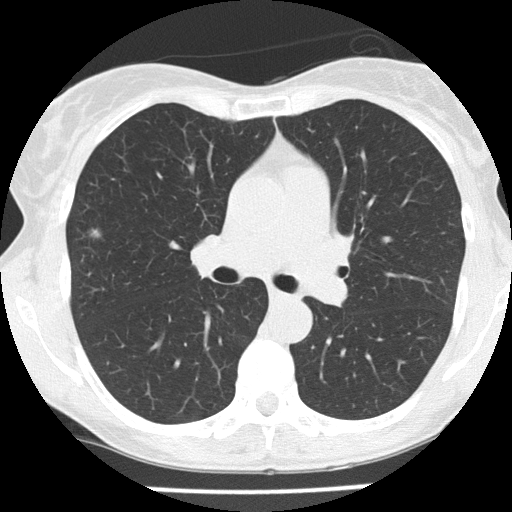
Chest CT (low-dose screening protocol), one axial image; first (baseline) screen; lung window (W 1500 / L -600 HU); 2 mm slice thickness; lung (sharp) reconstruction kernel (FC51); slice 64 of 166 in the series; 512 × 512 image matrix. Female participant, aged 56 years at enrolment. Former smoker at enrolment.
Expert-annotated lung lesion, bounding box [x1, y1, x2, y2] px = [80, 223, 118, 250]. Screening reader's record for this exam (one nodule recorded; not confirmed to be the boxed lesion): non-calcified nodule or mass ≥4 mm, right upper lobe, 7 × 5 mm, poorly defined margins, ground glass attenuation. Later outcome: lung cancer diagnosed 148 days after this screen — bronchiolo-alveolar carcinoma, non-mucinous, right upper lobe, well differentiated (G1), stage IA (AJCC 6th edition), 6 mm at pathology.